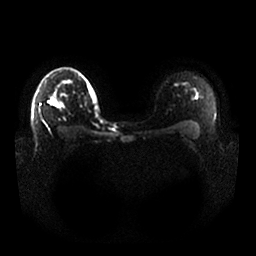
Breast MRI, one axial slice. Diffusion-weighted series; image 2 of 4 stored at this slice position (different b-values; order by instance number). 1.5 T. 4 mm slice thickness. 256 × 256 image matrix, field of view 370 × 370 mm. Female patient.
Structures marked on this image (expert manual segmentation):
- tumour on diffusion-weighted imaging: bounding box <49,101,58,107> (left, top, right, bottom; pixels)